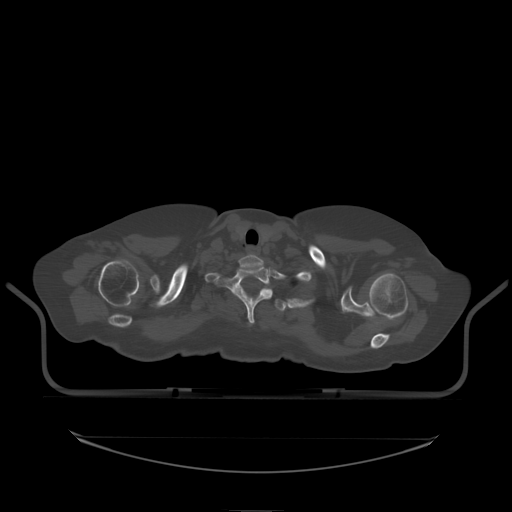
CT including the spine, one axial slice. Bone window (W 1800 / L 400 HU). 512 × 512 image matrix. Female patient, age 53 years. Case-level facts recorded for this patient, not image findings: primary cancer: lung.
Structures marked on this image (semi-automatically segmented with operator editing):
- T1 vertebra: box from (x=214, y=267) to (x=273, y=325) px
- T2 vertebra: (x=230, y=290)–(x=287, y=312)